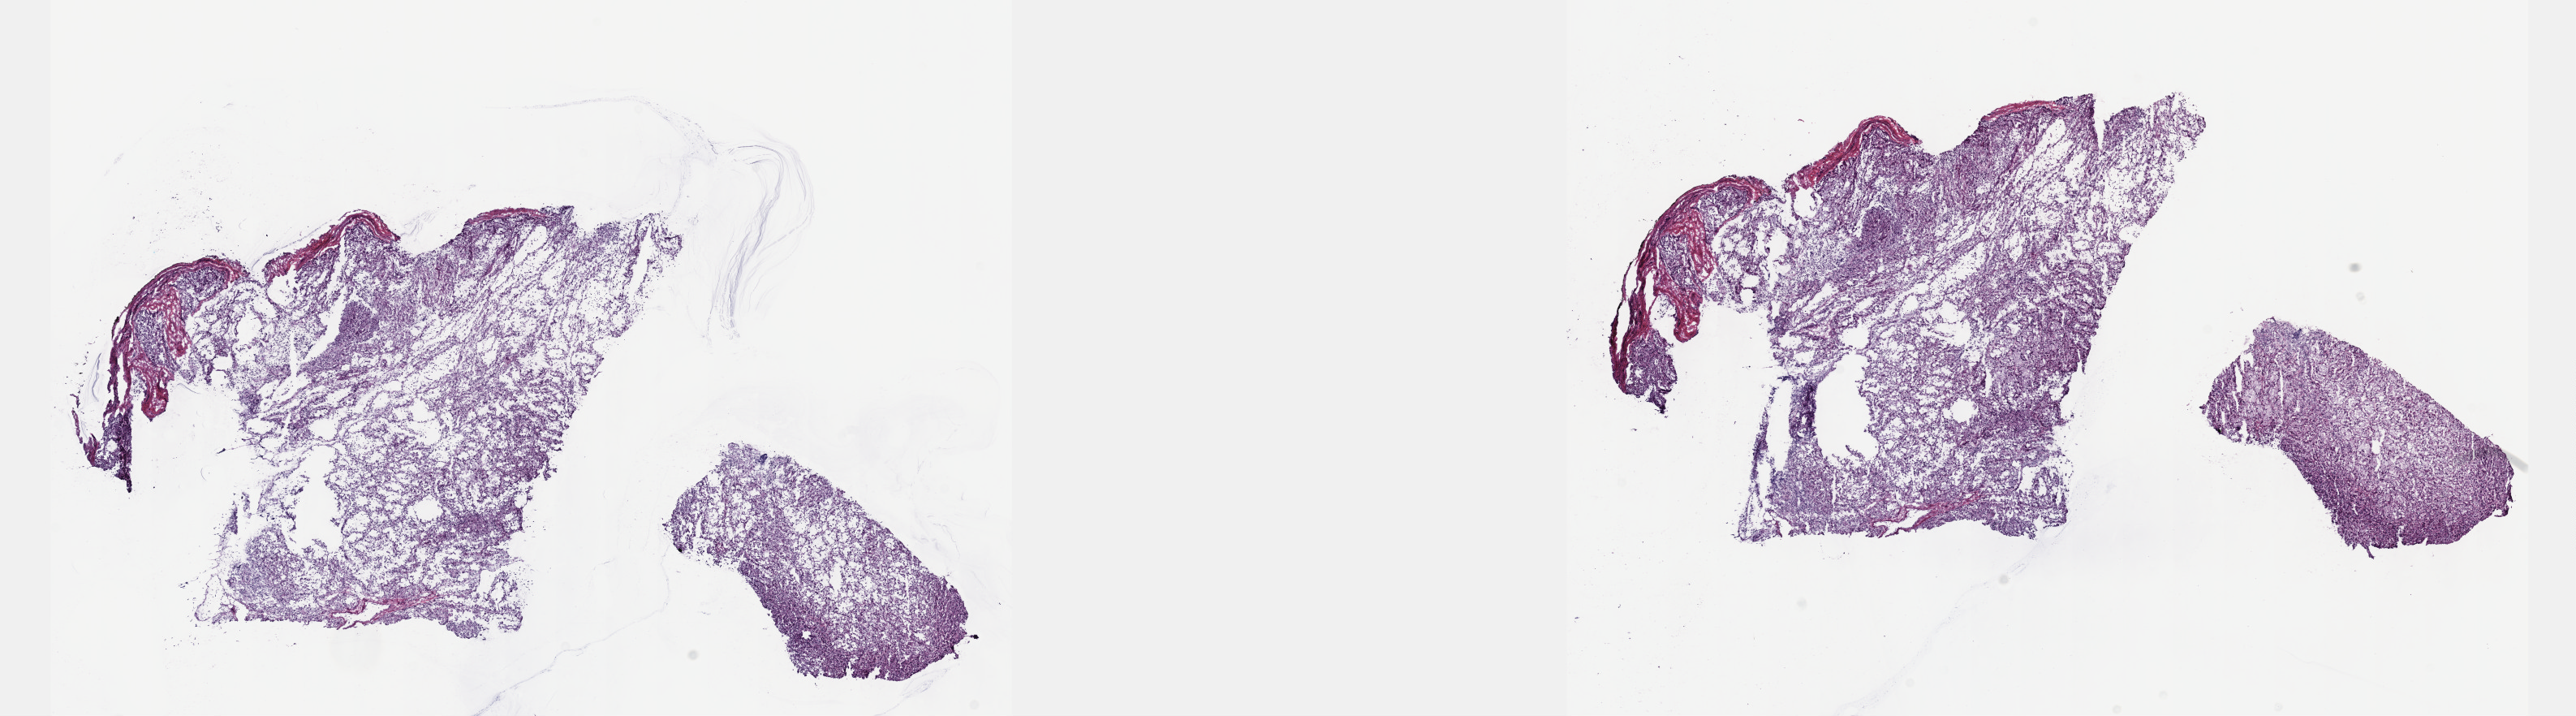
Hematoxylin and eosin (H&E) stained whole-slide image, low-resolution overview of the scanned area, about 25.7 x 7.1 mm. Frozen section from the top of the tissue portion. Primary tumour sample from the kidney. Female patient; age at initial diagnosis 60 years. Composition of this section per pathologist review: tumour cells 100%, tumour nuclei 75%, normal cells 0%, stromal cells 0%, necrosis 0%. Inflammatory infiltration, as recorded: lymphocyte infiltration 2%, monocyte infiltration 5%, neutrophil infiltration 0%.
Histologic diagnosis: Papillary adenocarcinoma, NOS. TNM: T1a NX MX. AJCC pathologic stage: I.